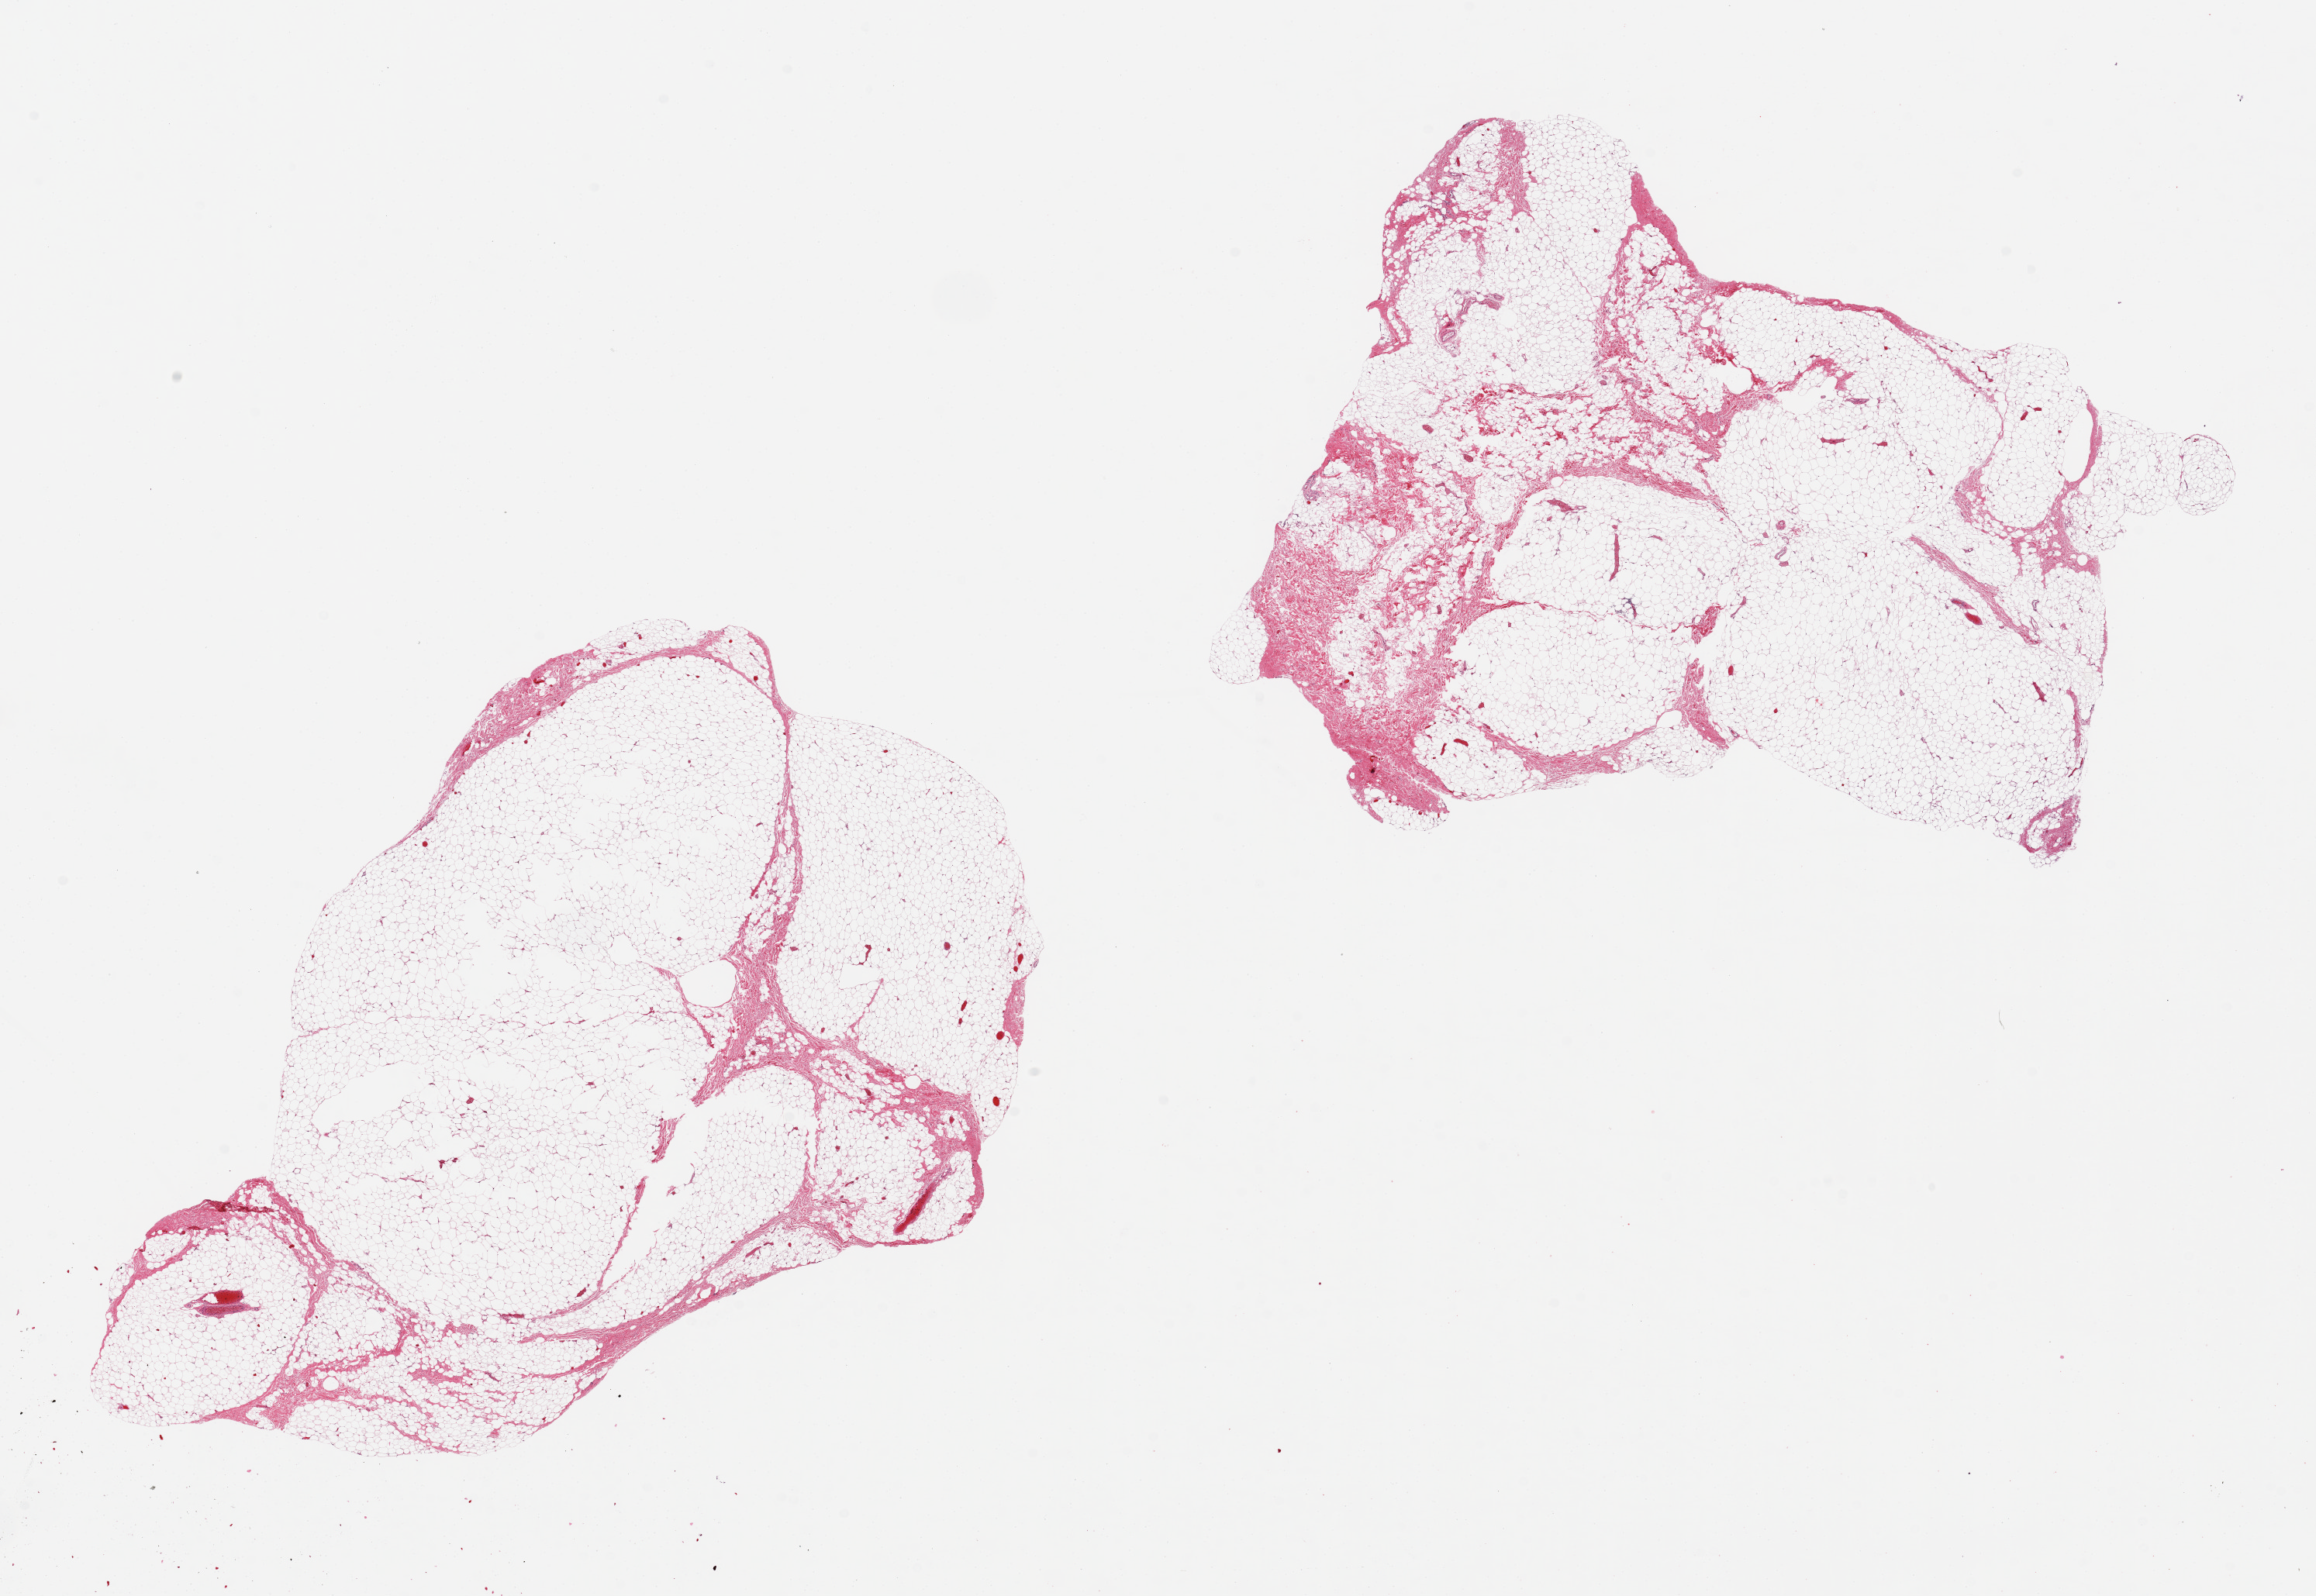
H&E whole-slide image, brightfield — whole scanned area (about 23.6 x 16.3 mm) shown as a low-resolution overview. PAXgene-fixed paraffin-embedded (PFPE) section. Target tissue: breast. Tissue donor sample. Male donor.
Pathologist's review note for this sample: 2 pieces ~9x5mm , all fat, no ductal elements visible.